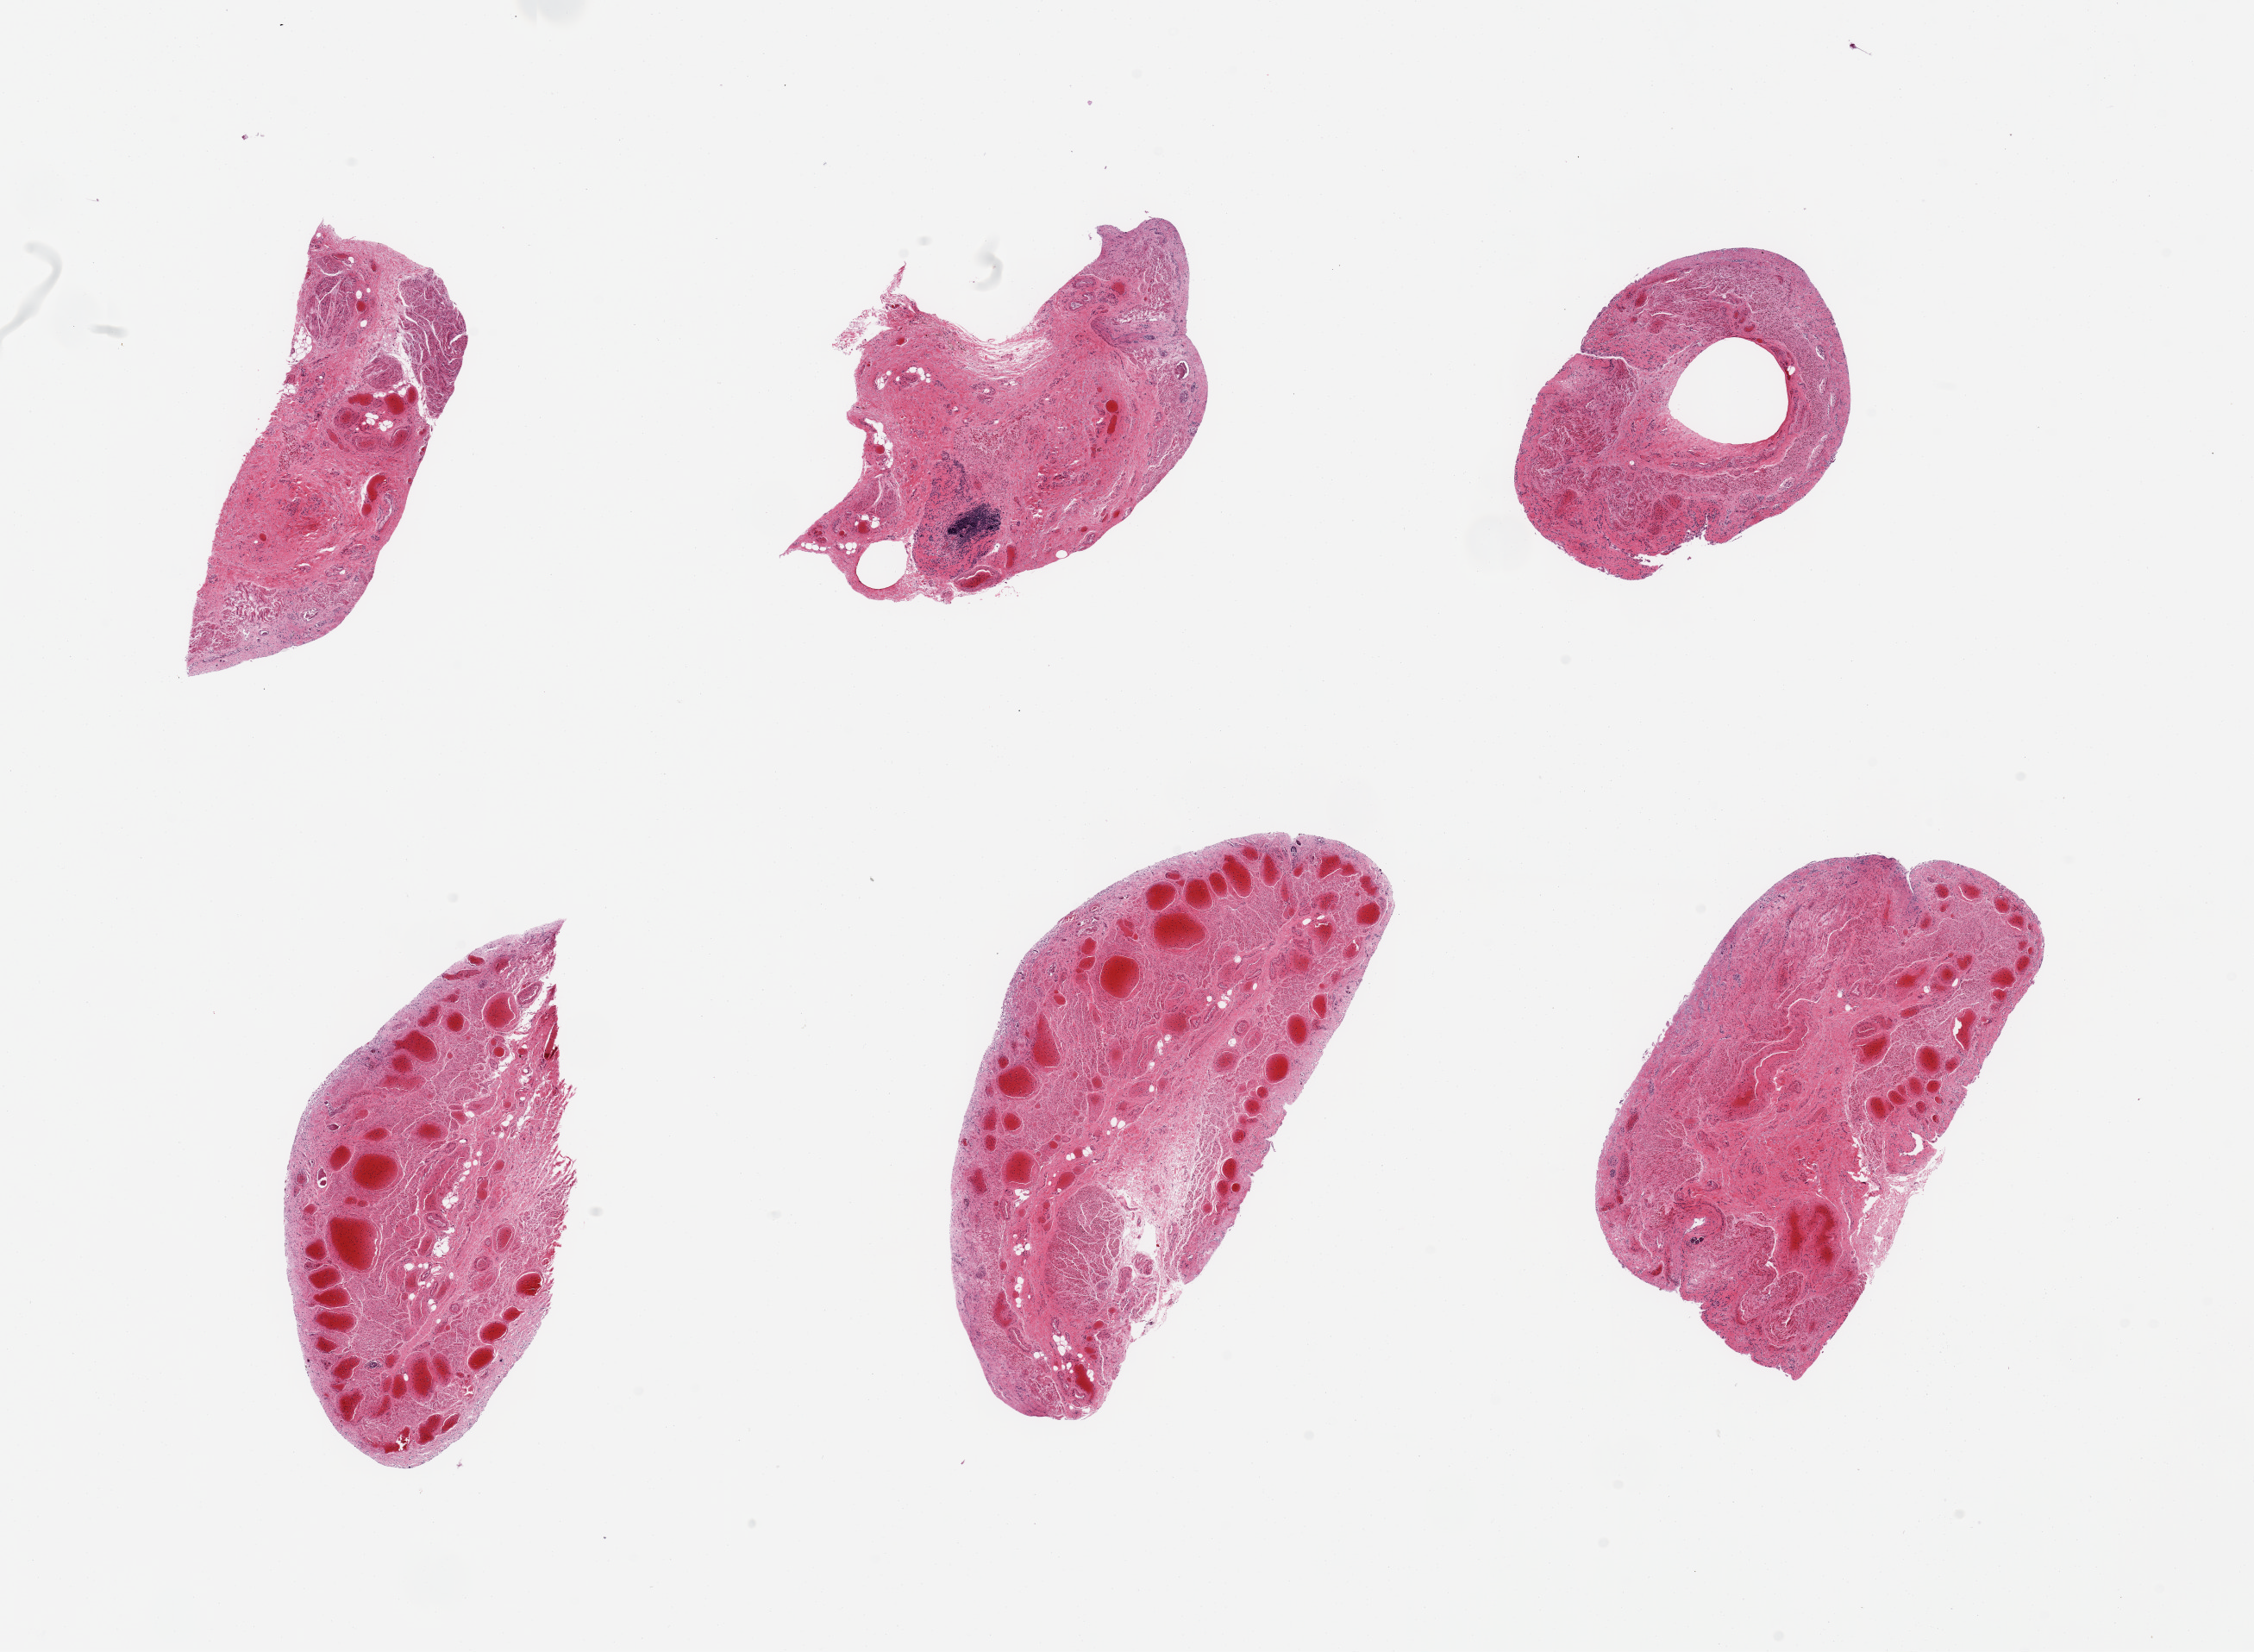
Whole-slide image, hematoxylin and eosin (H&E) stain, shown as a low-resolution overview of the whole scanned area (about 20.7 x 15.2 mm); PAXgene-fixed paraffin-embedded (PFPE) section; target tissue: gastroesophageal junction; tissue donor sample. Donor: female.
Review note (as recorded): 6 pieces; largely denuded mucosa and congested submucosa.